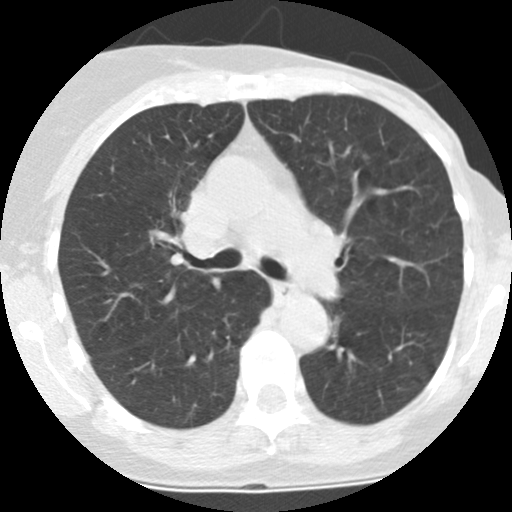
Chest CT (low-dose screening protocol), one axial image, baseline screening round, lung window (W 1500 / L -600 HU), 2.5 mm slice thickness, slice 90 of 225 in the series, 512 × 512 image matrix. Female, age 66 years at enrolment.
• Expert-annotated lung lesion, bounding box (x1, y1, x2, y2) in pixels: (358, 147, 375, 168).
• Screening reader's record for this exam: no non-calcified nodule ≥4 mm recorded.
• Lung cancer was diagnosed 583 days after this screen: adenocarcinoma, NOS, left lower lobe, poorly differentiated (G3), stage IA (AJCC 6th edition), 8 mm at pathology.